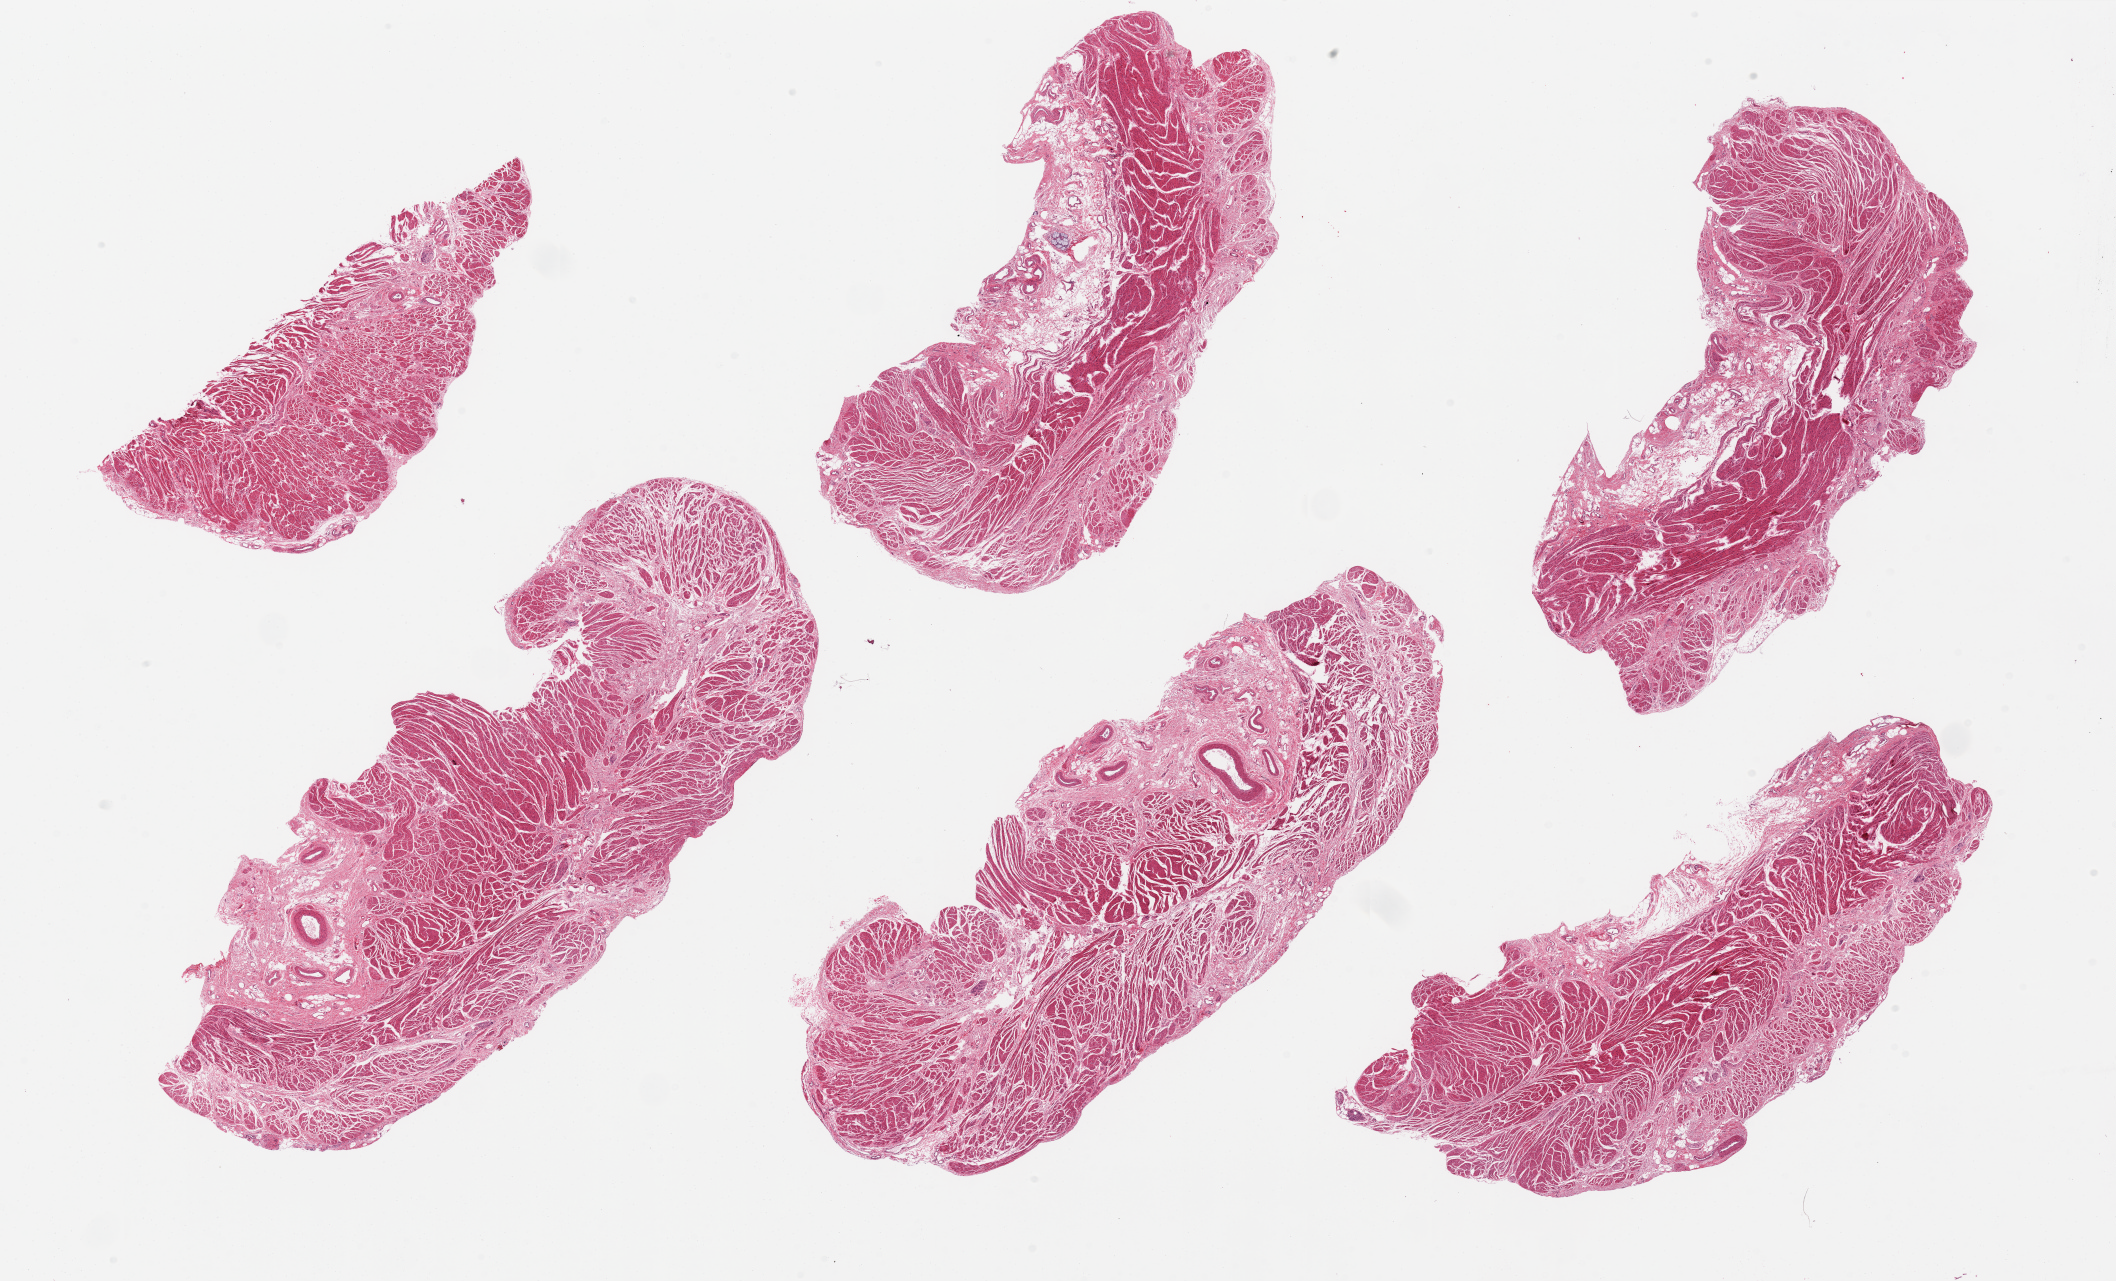
Haematoxylin and eosin whole-slide image, a low-resolution overview of the entire scanned area, about 33.5 x 20.3 mm; PAXgene-fixed, paraffin-embedded tissue; target tissue: gastroesophageal junction; tissue donor sample. Female donor.
Pathologist's review note for this sample: 6 pieces, well trimmed, few submucosal glands.